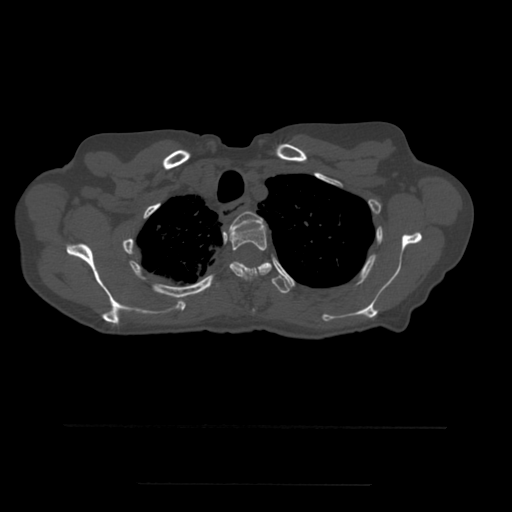
CT including the spine, one axial slice. Slice 419 of 544 in the series (ordered by position). Bone window (W 1800 / L 400 HU). 1.25 mm slice thickness. 512 × 512 image matrix, field of view 350 × 350 mm. Patient age 58 years. From the clinical record (not read from this slice): primary cancer: lung.
Structures marked on this image (semi-automatically segmented with operator editing):
- T2 vertebra: bounding box <224,212,263,239> (left, top, right, bottom; pixels)
- T3 vertebra: <230,224,272,283>
- T4 vertebra: <231,262,292,294>